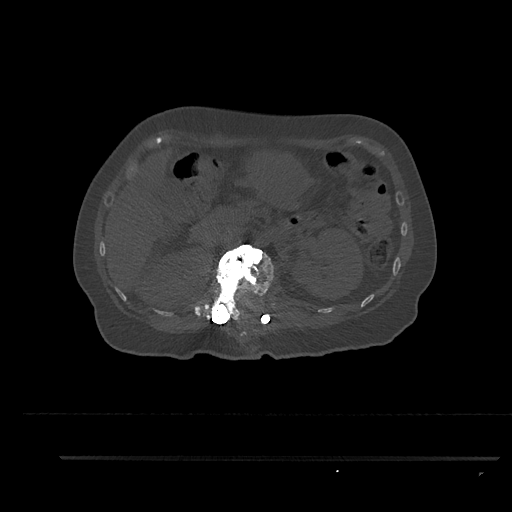
CT including the spine, one axial slice; slice 224 of 797 in the series (ordered by position); reconstruction kernel Br40s/3; 120 kVp; bone window (W 1800 / L 400 HU); 0.5 mm slice thickness; 512 × 512 image matrix, field of view 408 × 408 mm. Female patient, age 44 years. Case-level facts recorded for this patient, not image findings: primary cancer: renal.
Outlined on this slice (semi-automatically segmented with operator editing):
- L1 vertebra: bounding box [x1, y1, x2, y2] px = [207, 244, 274, 321]
- T12 vertebra: [243, 331, 247, 336]